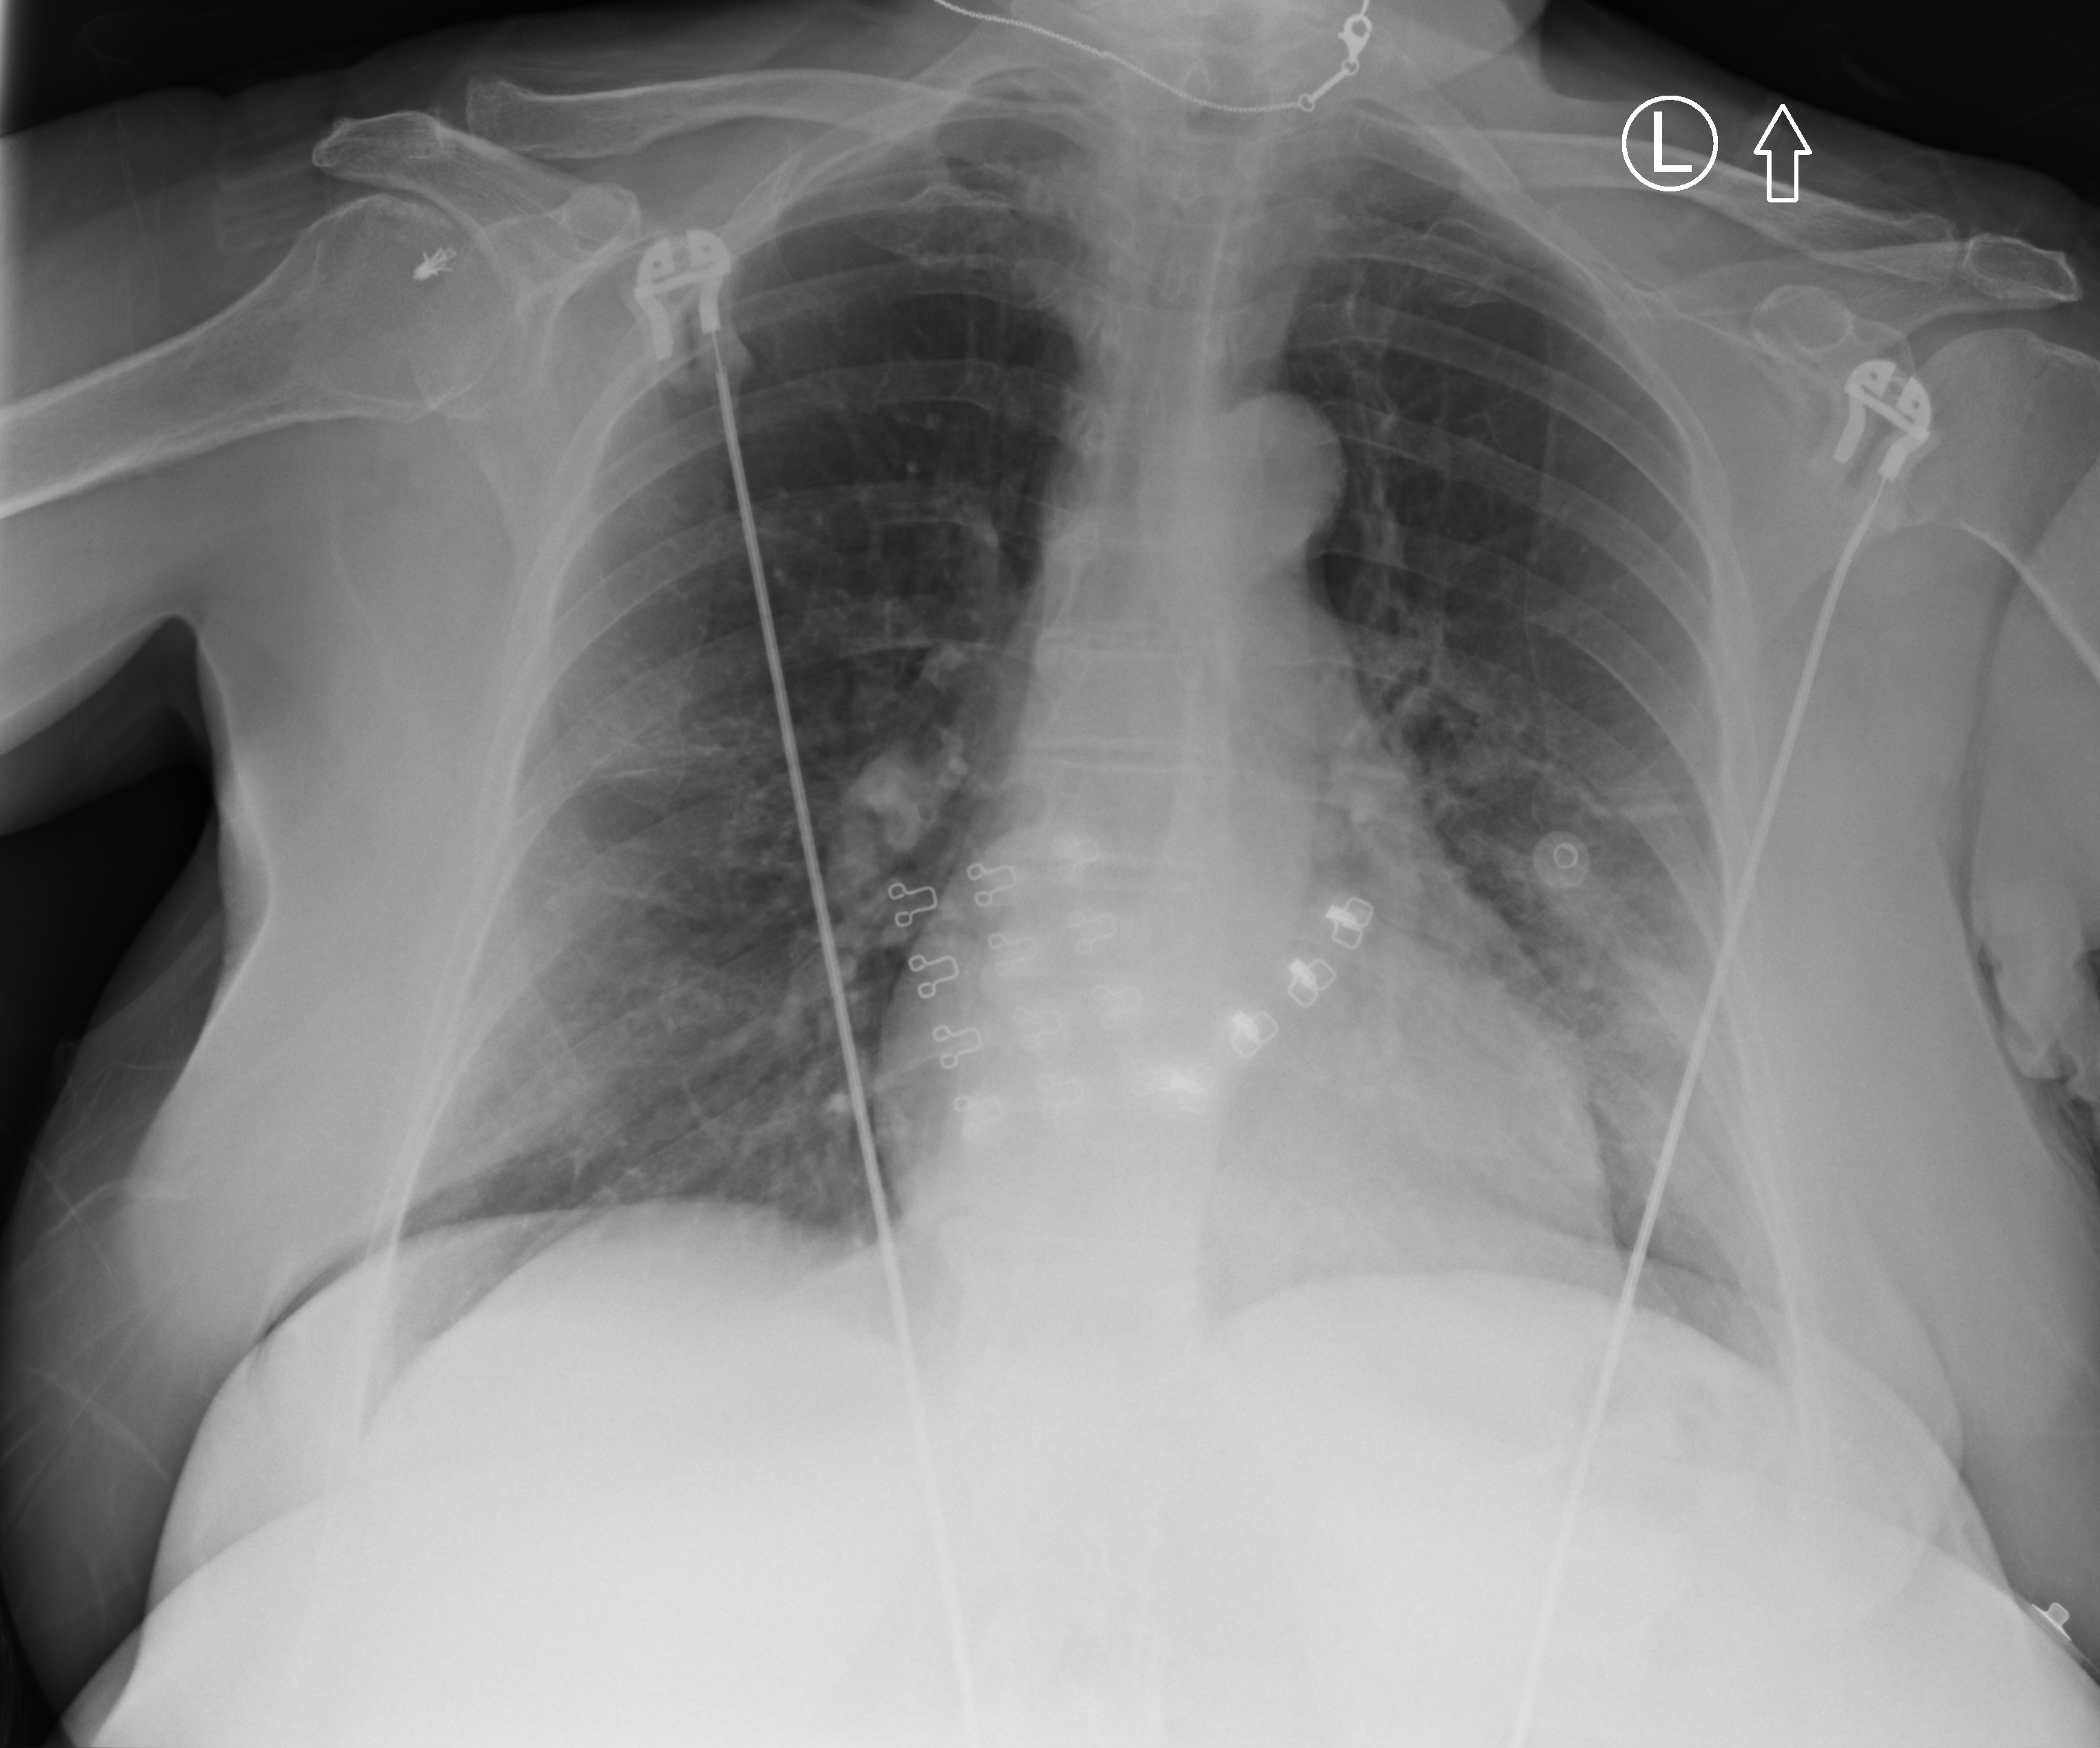
Bedside chest radiograph (computed radiography), anteroposterior (AP) projection. Patient hospitalised with COVID-19; female, aged 60–74 years.
Admission-level facts for this patient (not findings on this image; timing relative to this image not recorded):
- mechanically ventilated during this hospital stay: no